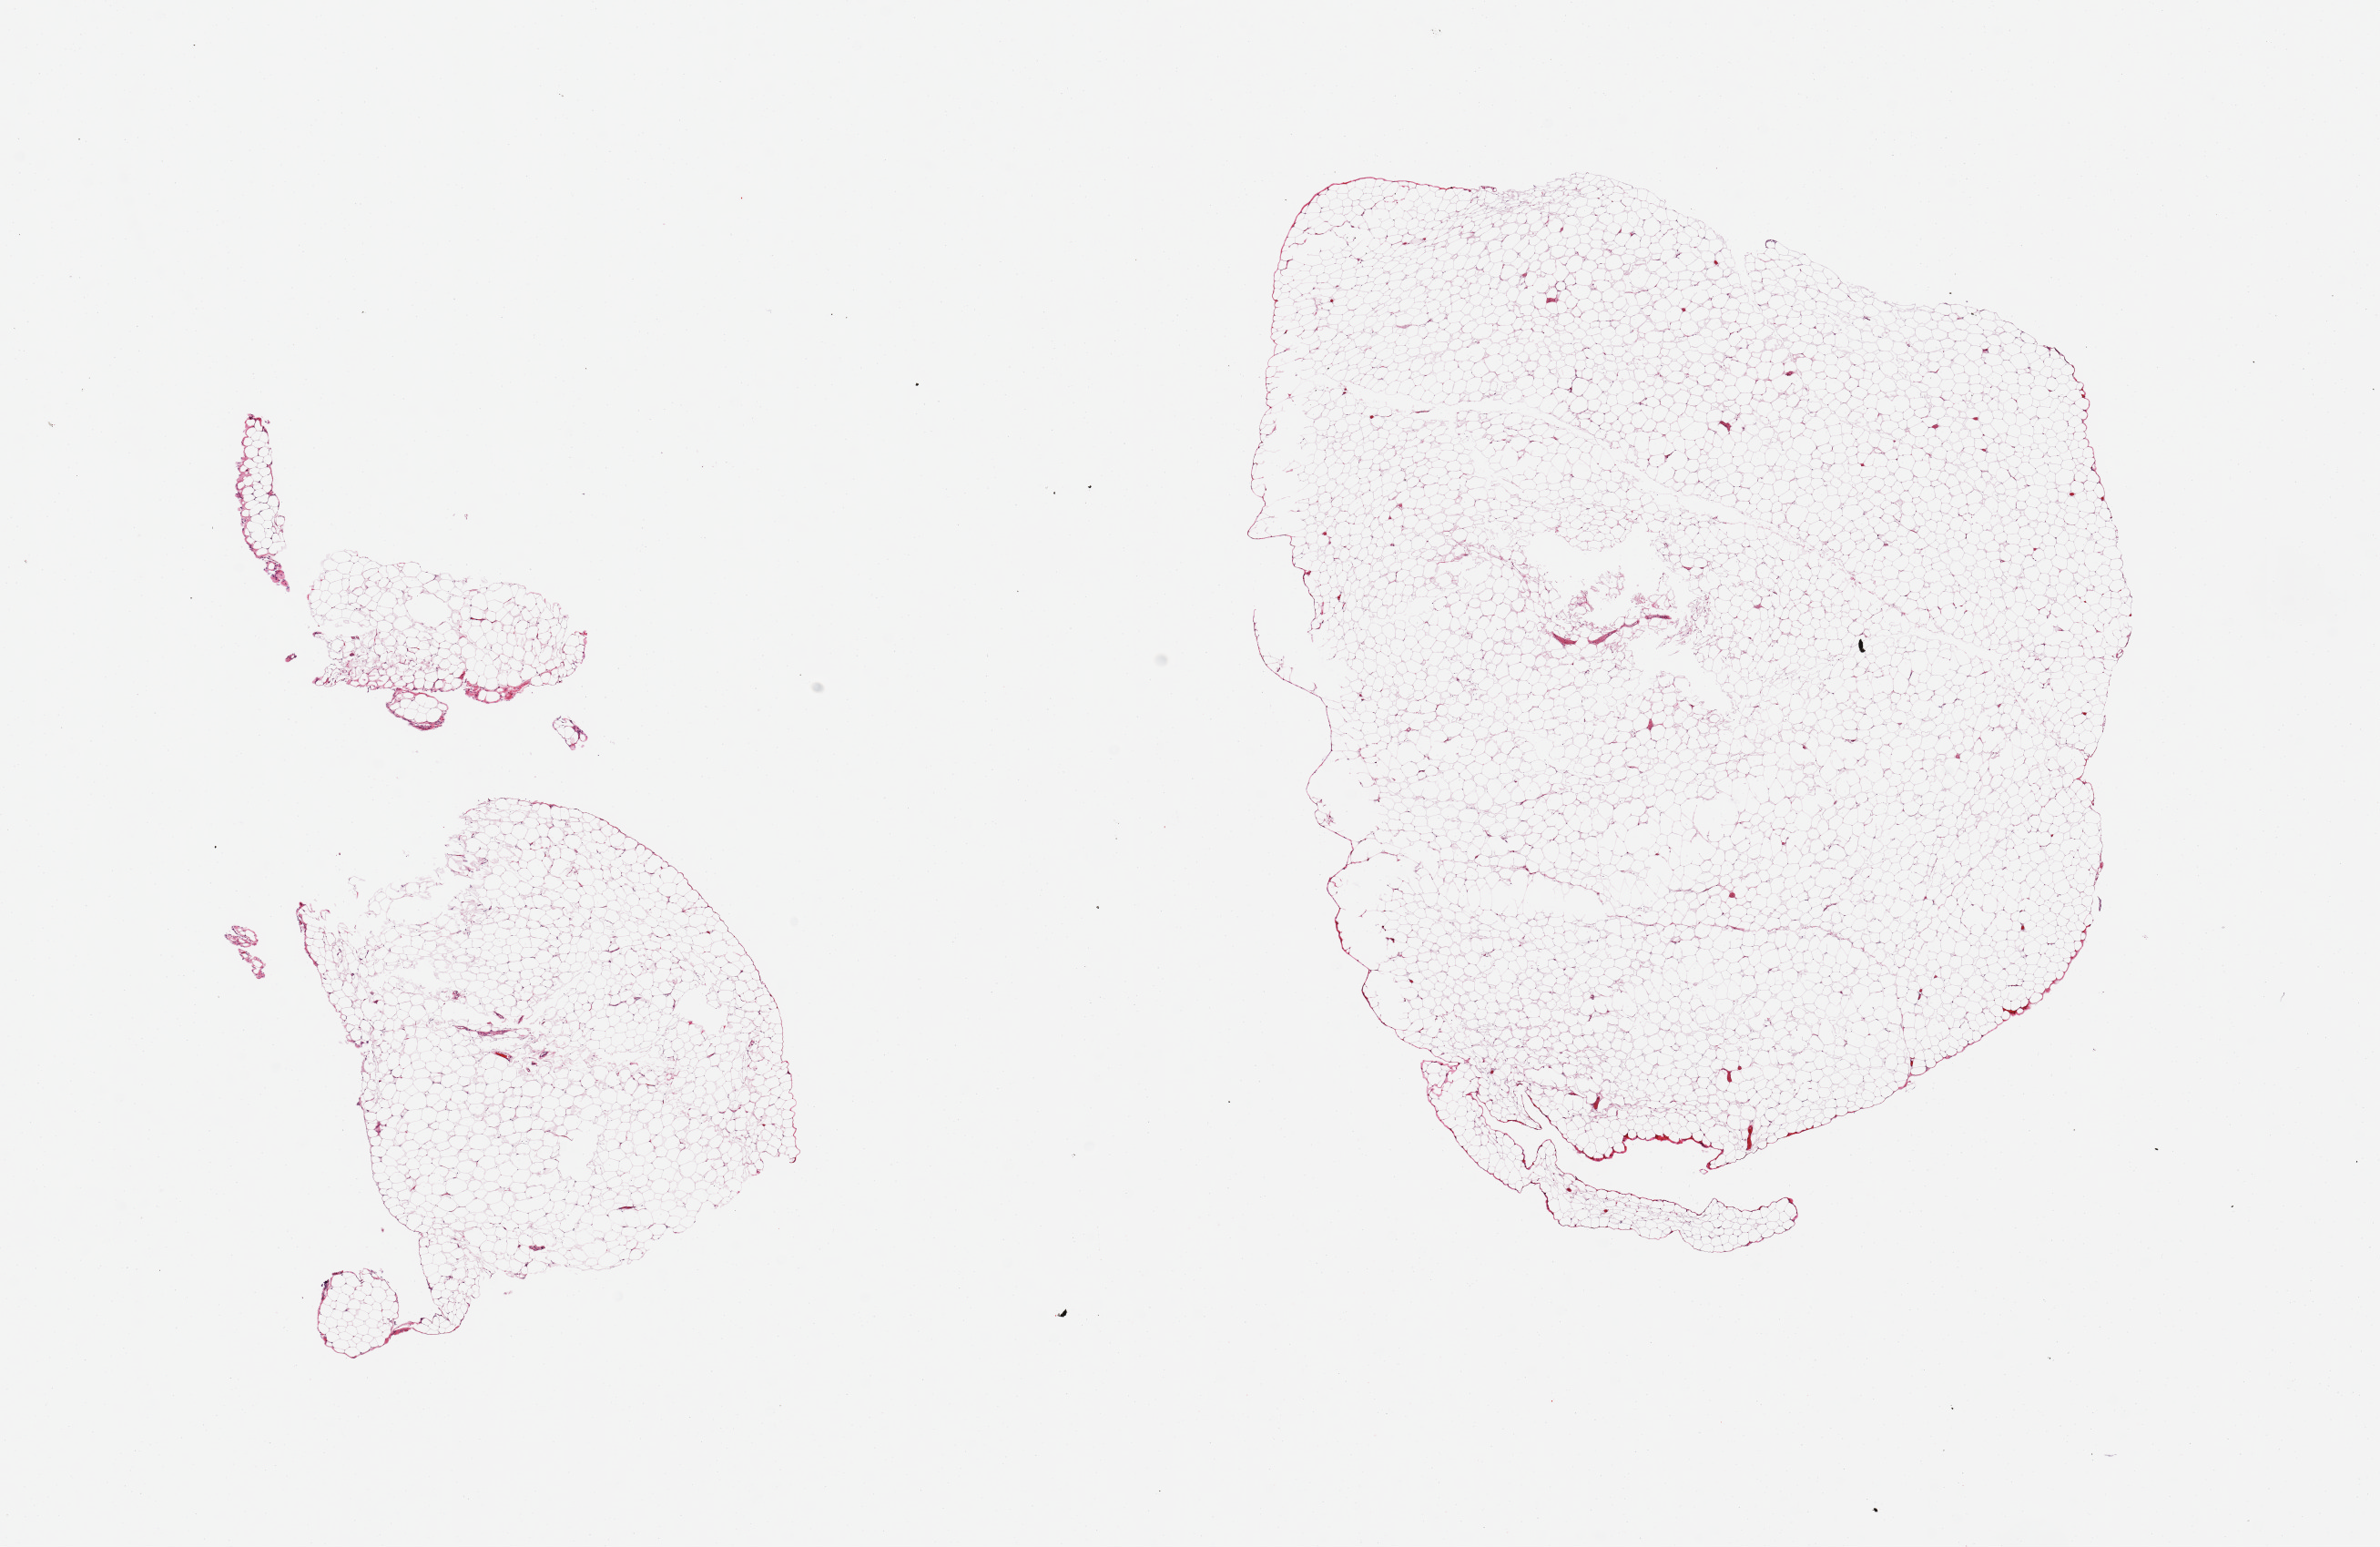
H&E whole-slide image, brightfield, shown as a low-resolution overview of the whole scanned area (about 20.7 x 13.4 mm), PAXgene-fixed, paraffin-embedded tissue, sampled site (target tissue): omentum, tissue donor sample. Donor sex: male.
Review note (as recorded): 2 pieces, only trace fascia/vascular elements.